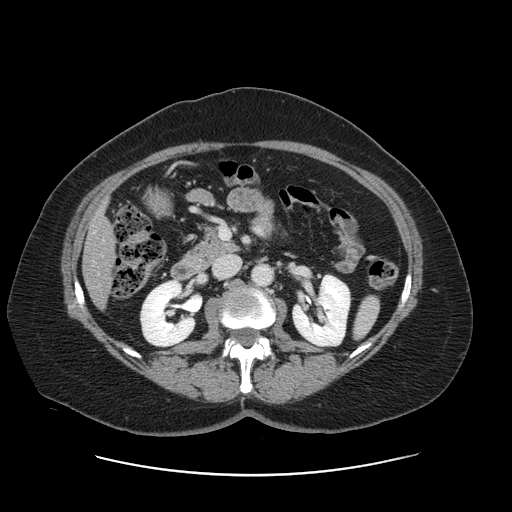
Contrast-enhanced abdominal CT, one axial slice; slice 54 of 161 in the series (ordered by position); intravenous contrast given; soft-tissue window (W 400 / L 40 HU); 512 × 512 image matrix, field of view 398 × 398 mm. Female patient, age 62 years. Case-level facts recorded for this patient, not image findings: diagnosis: colorectal cancer liver metastases, imaged before liver resection; multiple liver metastases: no.
Structures marked on this image (outlined manually by an expert reader):
- liver: box from (x=84, y=211) to (x=113, y=305) px